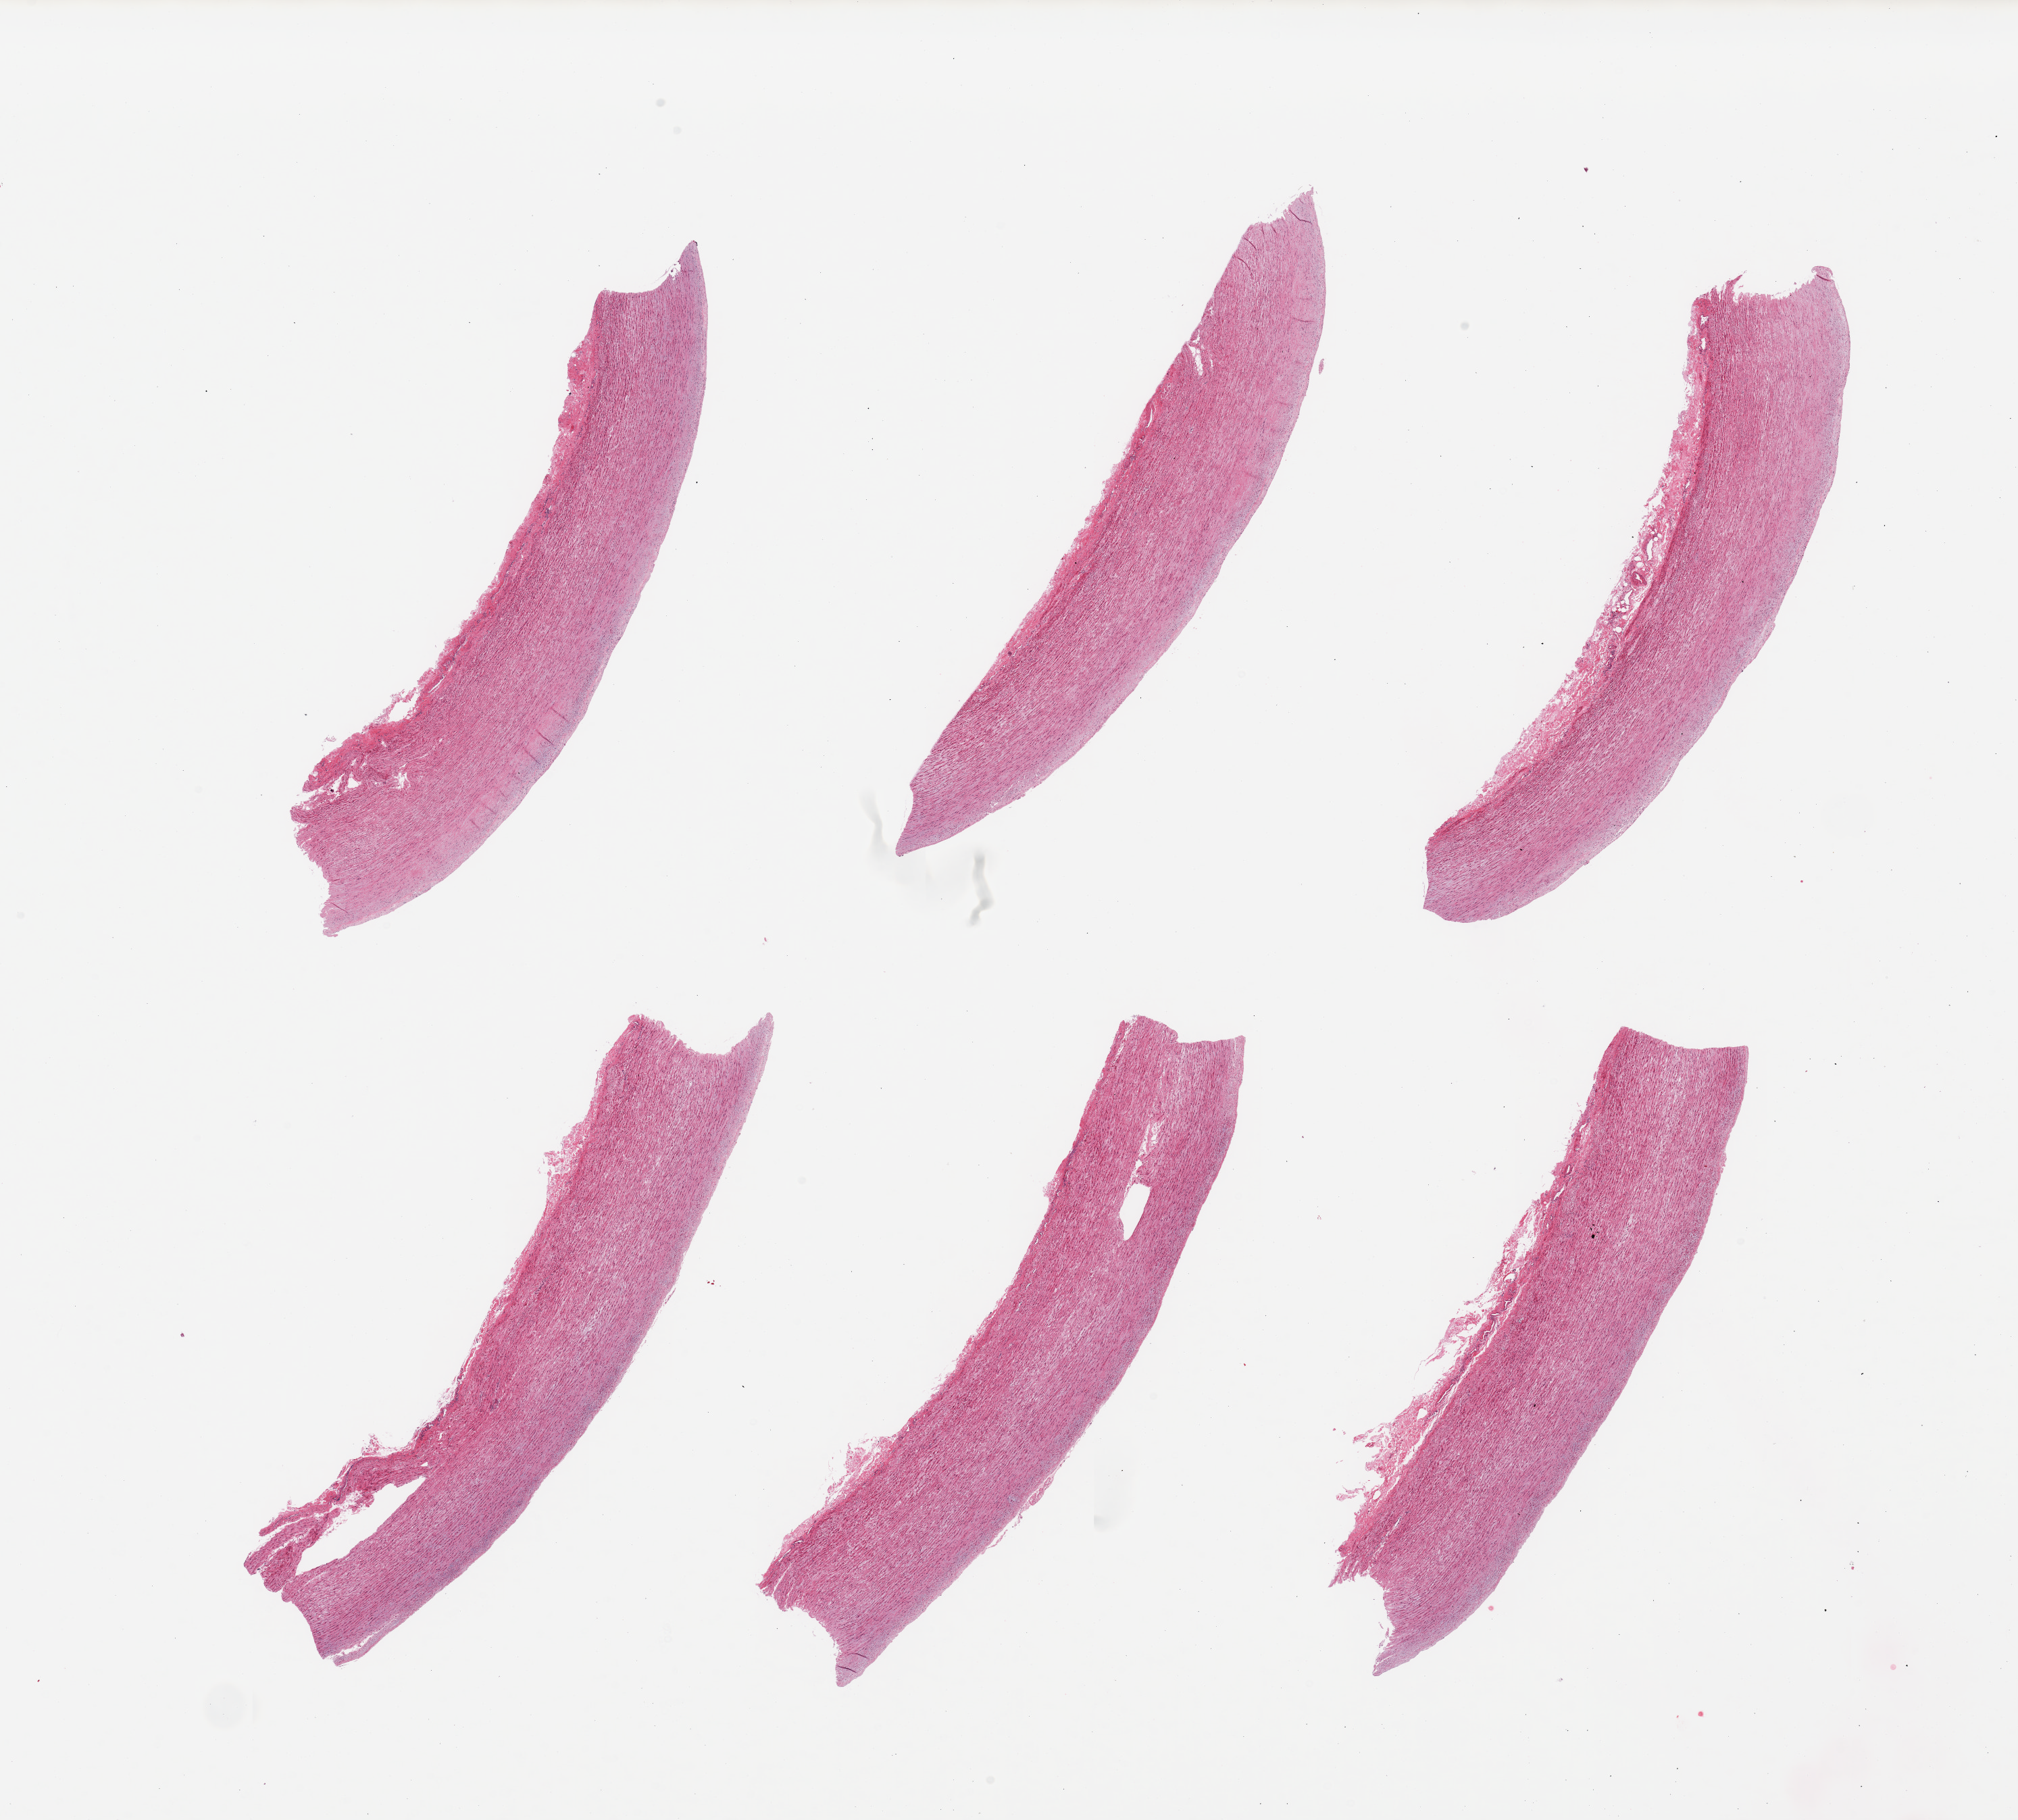
Digitized hematoxylin and eosin (H&E)-stained section, whole scanned area (about 23.6 x 21.3 mm, from a 20x scan) shown as a low-resolution overview, PAXgene-fixed, paraffin-embedded tissue, sampled site (target tissue): aorta, tissue donor sample.
Review note (as recorded): 6 pieces; early atherosis and trace of adventitia.